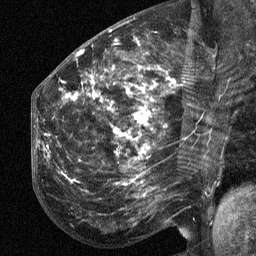
Breast MRI (dynamic contrast-enhanced), one sagittal slice. Dynamic contrast-enhanced study with each time point stored as its own series, time point 2 of 3 at this slice position (early post-contrast, ordered by acquisition time). 1.5 T. TE 4.8 ms, TR 27 ms. 2.3 mm slice thickness. 256 × 256 image matrix. Patient: female, 50 years. From the clinical record (not read from this slice): setting: breast cancer imaged before/during neoadjuvant chemotherapy; receptor status: HER2-positive.
Structures marked on this image (semi-automatic segmentation, software-assisted and operator-edited):
- analysis volume of interest (the breast-tissue region the enhancement analysis was run in; not a lesion): bounding box [x1, y1, x2, y2] px = [53, 64, 211, 215]
- tumour enhancement mask (voxels above the 90 % enhancement threshold inside the analysis volume of interest): [66, 76, 150, 182]